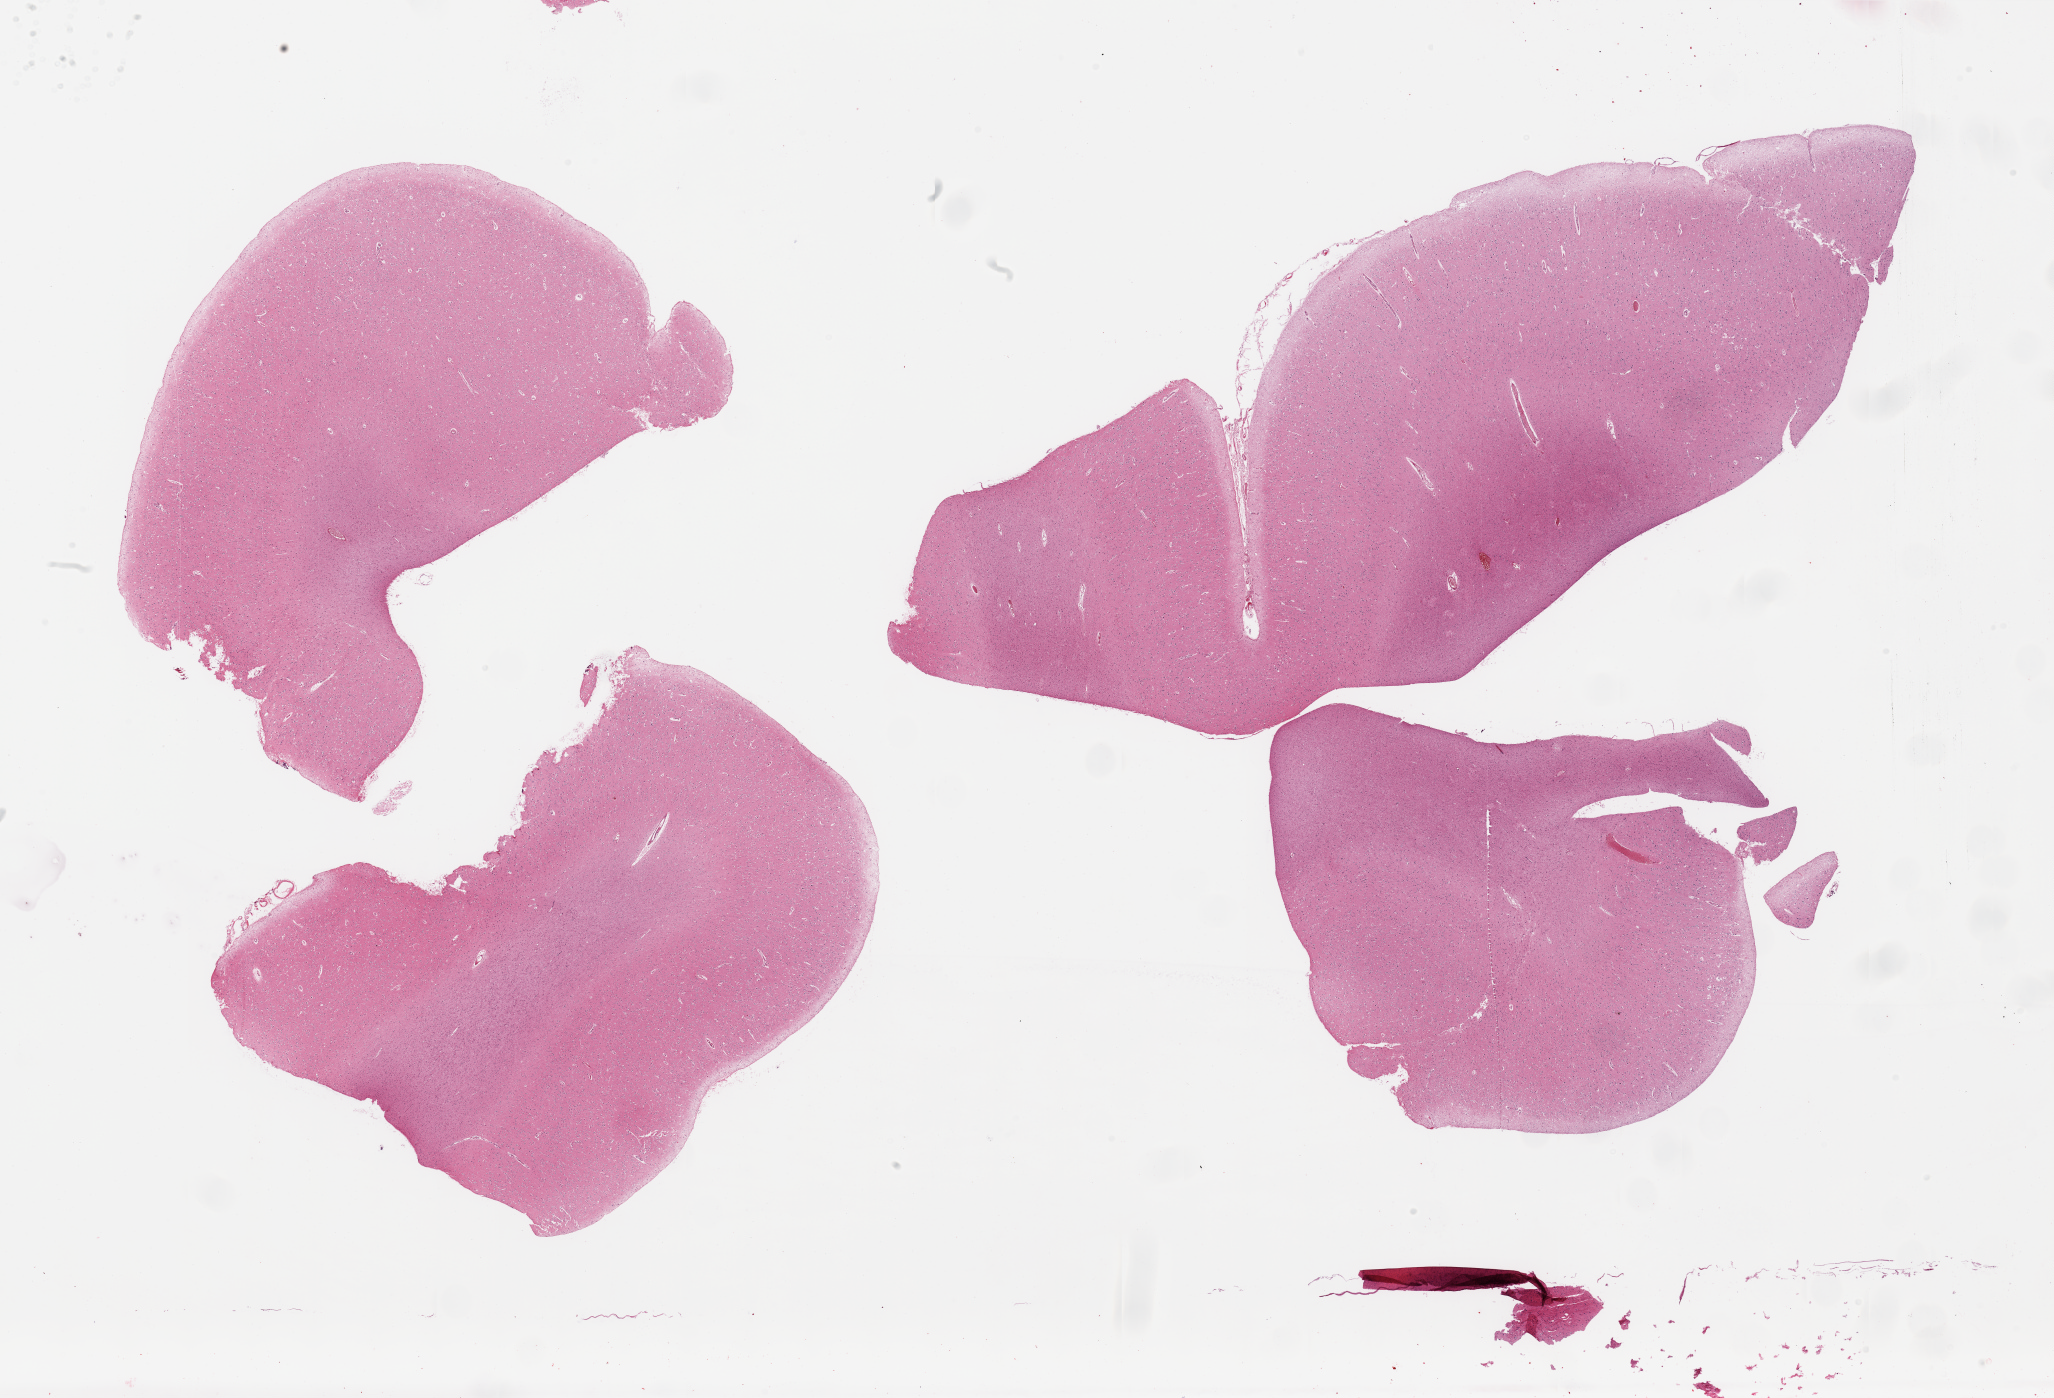
Digitized H&E-stained section, low-resolution overview of the scanned area, about 32.5 x 22.1 mm (slide scanned at 20x); PAXgene-fixed, paraffin-embedded tissue; section of cerebral cortex (target tissue); donor tissue sample. Male donor.
Reviewer comment on this tissue sample: 4 pieces; outer, convex edges appear pale: possible artifact (not seen in cerebellum).